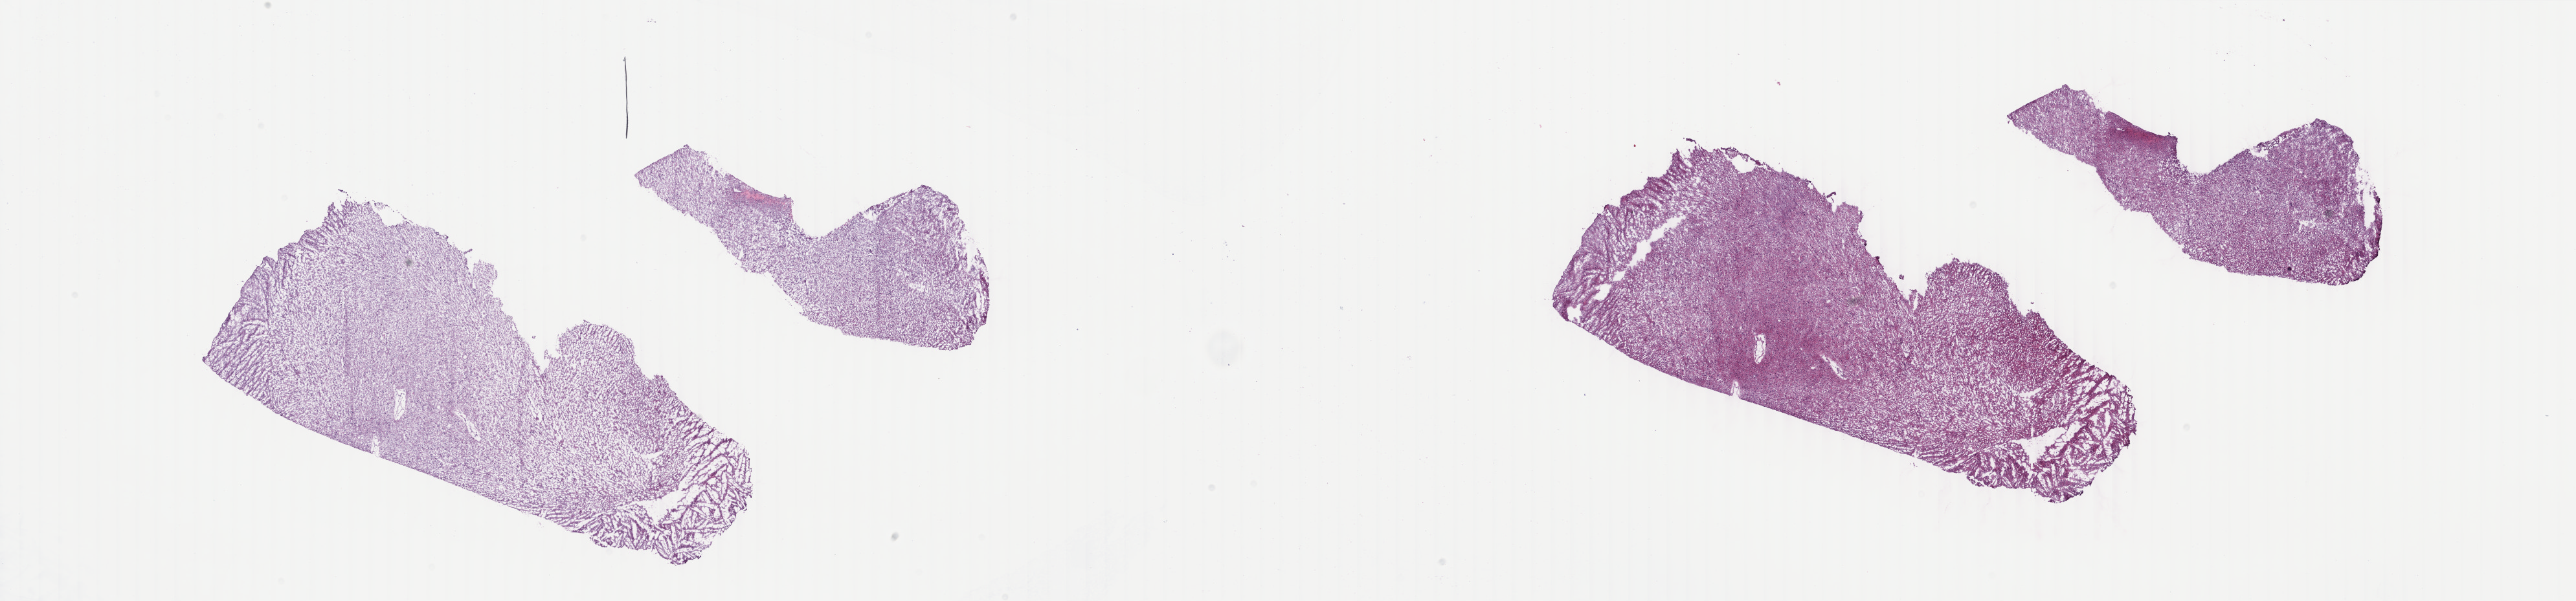
Digitized H&E-stained tissue section (whole slide), a low-resolution overview of the entire scanned area, about 31.6 x 7.4 mm (from a 40x scan); frozen section; brain, primary tumour sample. Male, age 25 years at initial diagnosis. Histologic grade: G2 (moderately differentiated). Slide review estimates, as recorded: tumour cells 30%, tumour nuclei 80%, normal cells 10%, stromal cells 60%, necrosis 0%. Inflammatory infiltration, as recorded: lymphocyte infiltration 0%, monocyte infiltration 0%, neutrophil infiltration 0%.
Histologic diagnosis: Oligodendroglioma, NOS (cerebrum).